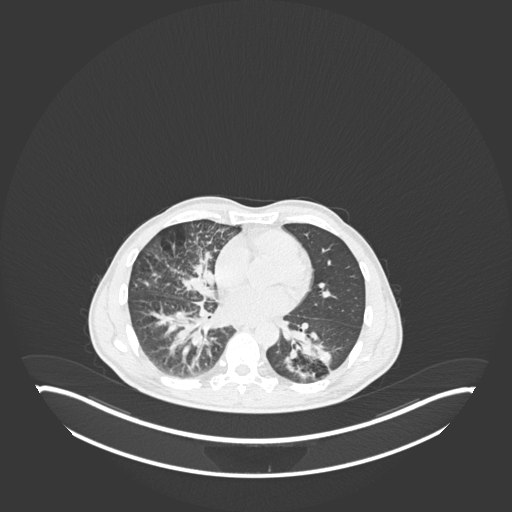
Chest CT, one axial slice; position 104 of 237 along the scan axis; 120 kVp; lung window (W 1500 / L -600 HU); 1 mm slice thickness; 512 × 512 image matrix, field of view 500 × 500 mm. Patient: male, 49 years. Case-level facts recorded for this patient, not image findings: clinical TNM (as recorded): T2b N1 M0.
Outlined on this slice (bounding box drawn by a radiologist):
- lung tumour (recorded histology: adenocarcinoma): bounding box [x1, y1, x2, y2] px = [276, 328, 333, 384]